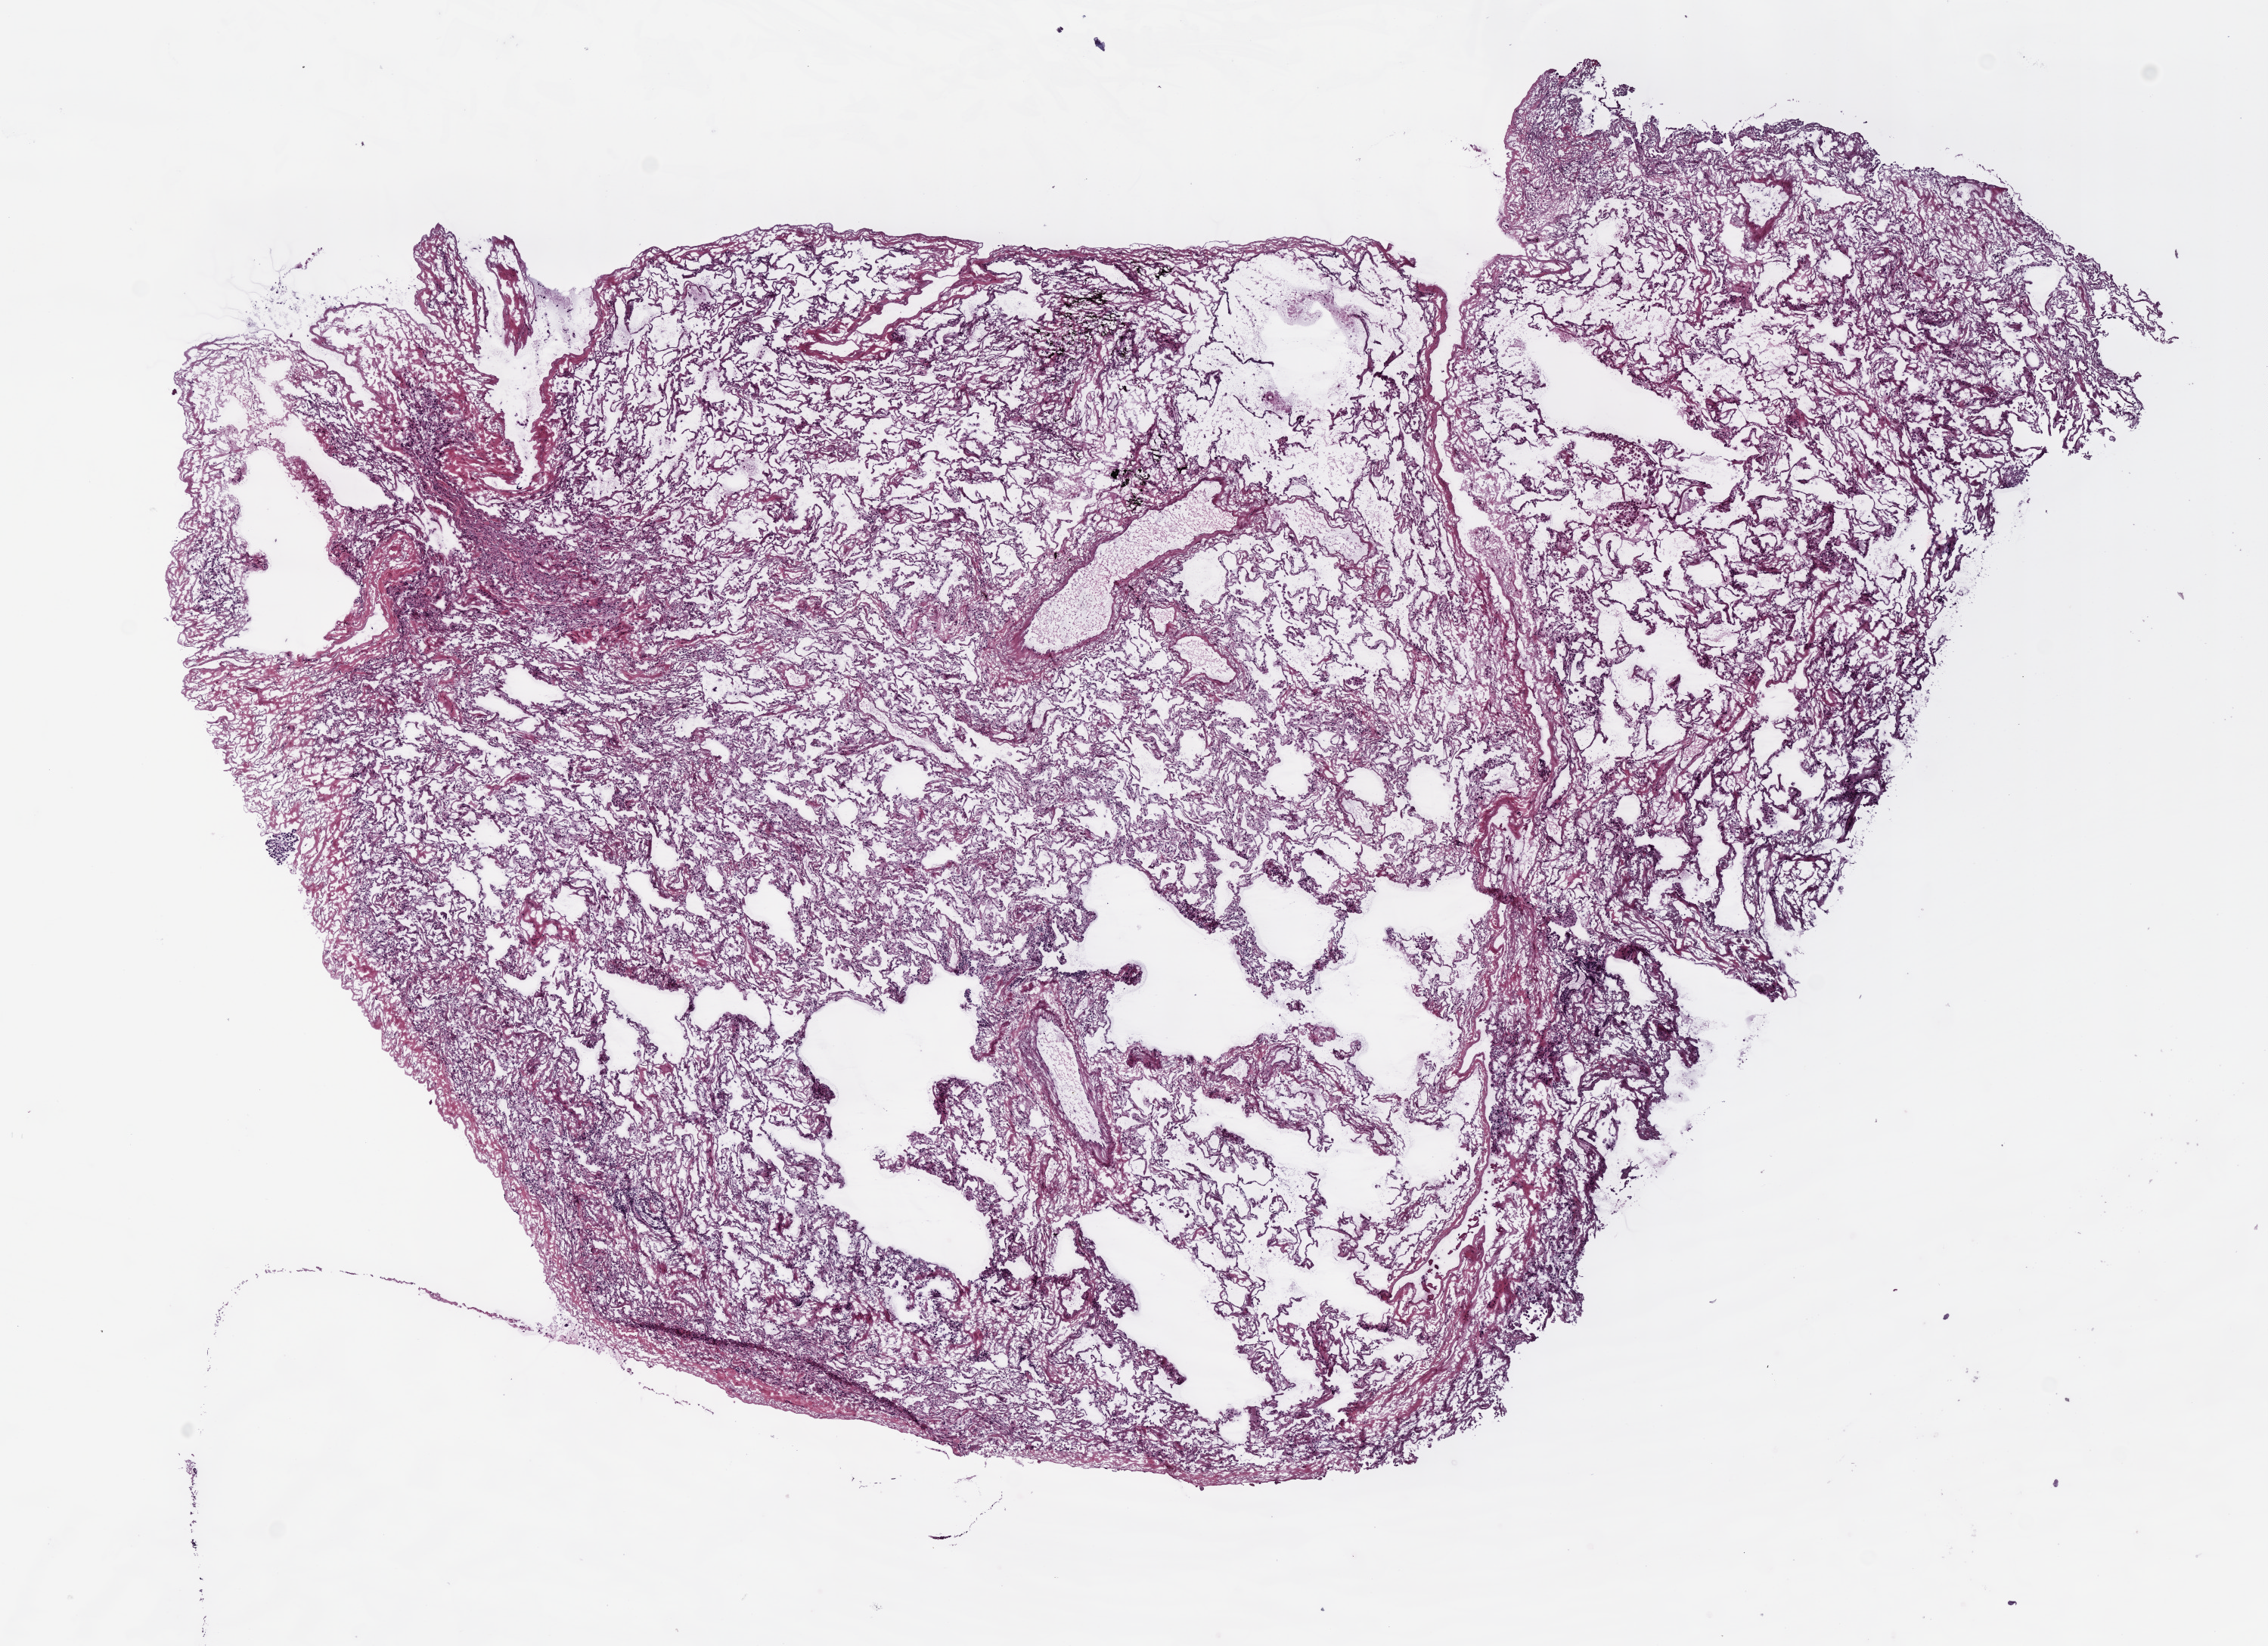
Digitized H&E-stained tissue section (whole slide), shown as a low-resolution overview of the whole scanned area (about 12.0 x 8.7 mm, from a 20x scan). Frozen section. Lung, solid tissue normal (non-tumour tissue) sample. Patient: female, age at initial diagnosis 76 years.
This section: solid tissue normal sample (biorepository sample class). Patient diagnosis: Adenocarcinoma with mixed subtypes.